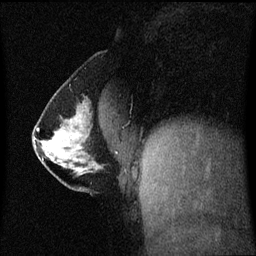
Breast MRI (dynamic contrast-enhanced), one sagittal slice; slice 27 of 60 in the series (ordered by position); dynamic contrast-enhanced series, image 2 of 3 at this slice position (ordered by acquisition); 1.5 T; TE 4.2 ms, TR 8.4 ms; 256 × 256 image matrix. Patient: female, 40 years. Case-level facts recorded for this patient, not image findings: setting: breast cancer imaged before/during neoadjuvant chemotherapy; receptor status: triple-negative.
Outlined on this slice (semi-automatic segmentation, software-assisted and operator-edited):
- analysis volume of interest (the breast-tissue region the enhancement analysis was run in; not a lesion): bounding box <33,112,106,188> (left, top, right, bottom; pixels)
- tumour enhancement mask (voxels above the 70 % enhancement threshold inside the analysis volume of interest): <38,129,78,146>